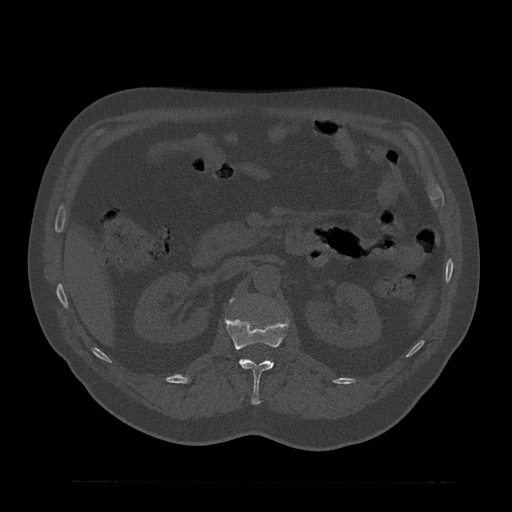
CT including the spine, one axial slice. Reconstruction kernel Br40s/3. 120 kVp. Bone window (W 1800 / L 400 HU). 512 × 512 image matrix, field of view 430 × 430 mm. Patient: male, 61 years. From the clinical record (not read from this slice): primary cancer: prostate.
Outlined on this slice (semi-automatically segmented with operator editing):
- L1 vertebra: bounding box (x1, y1, x2, y2) in pixels: (212, 317, 289, 405)